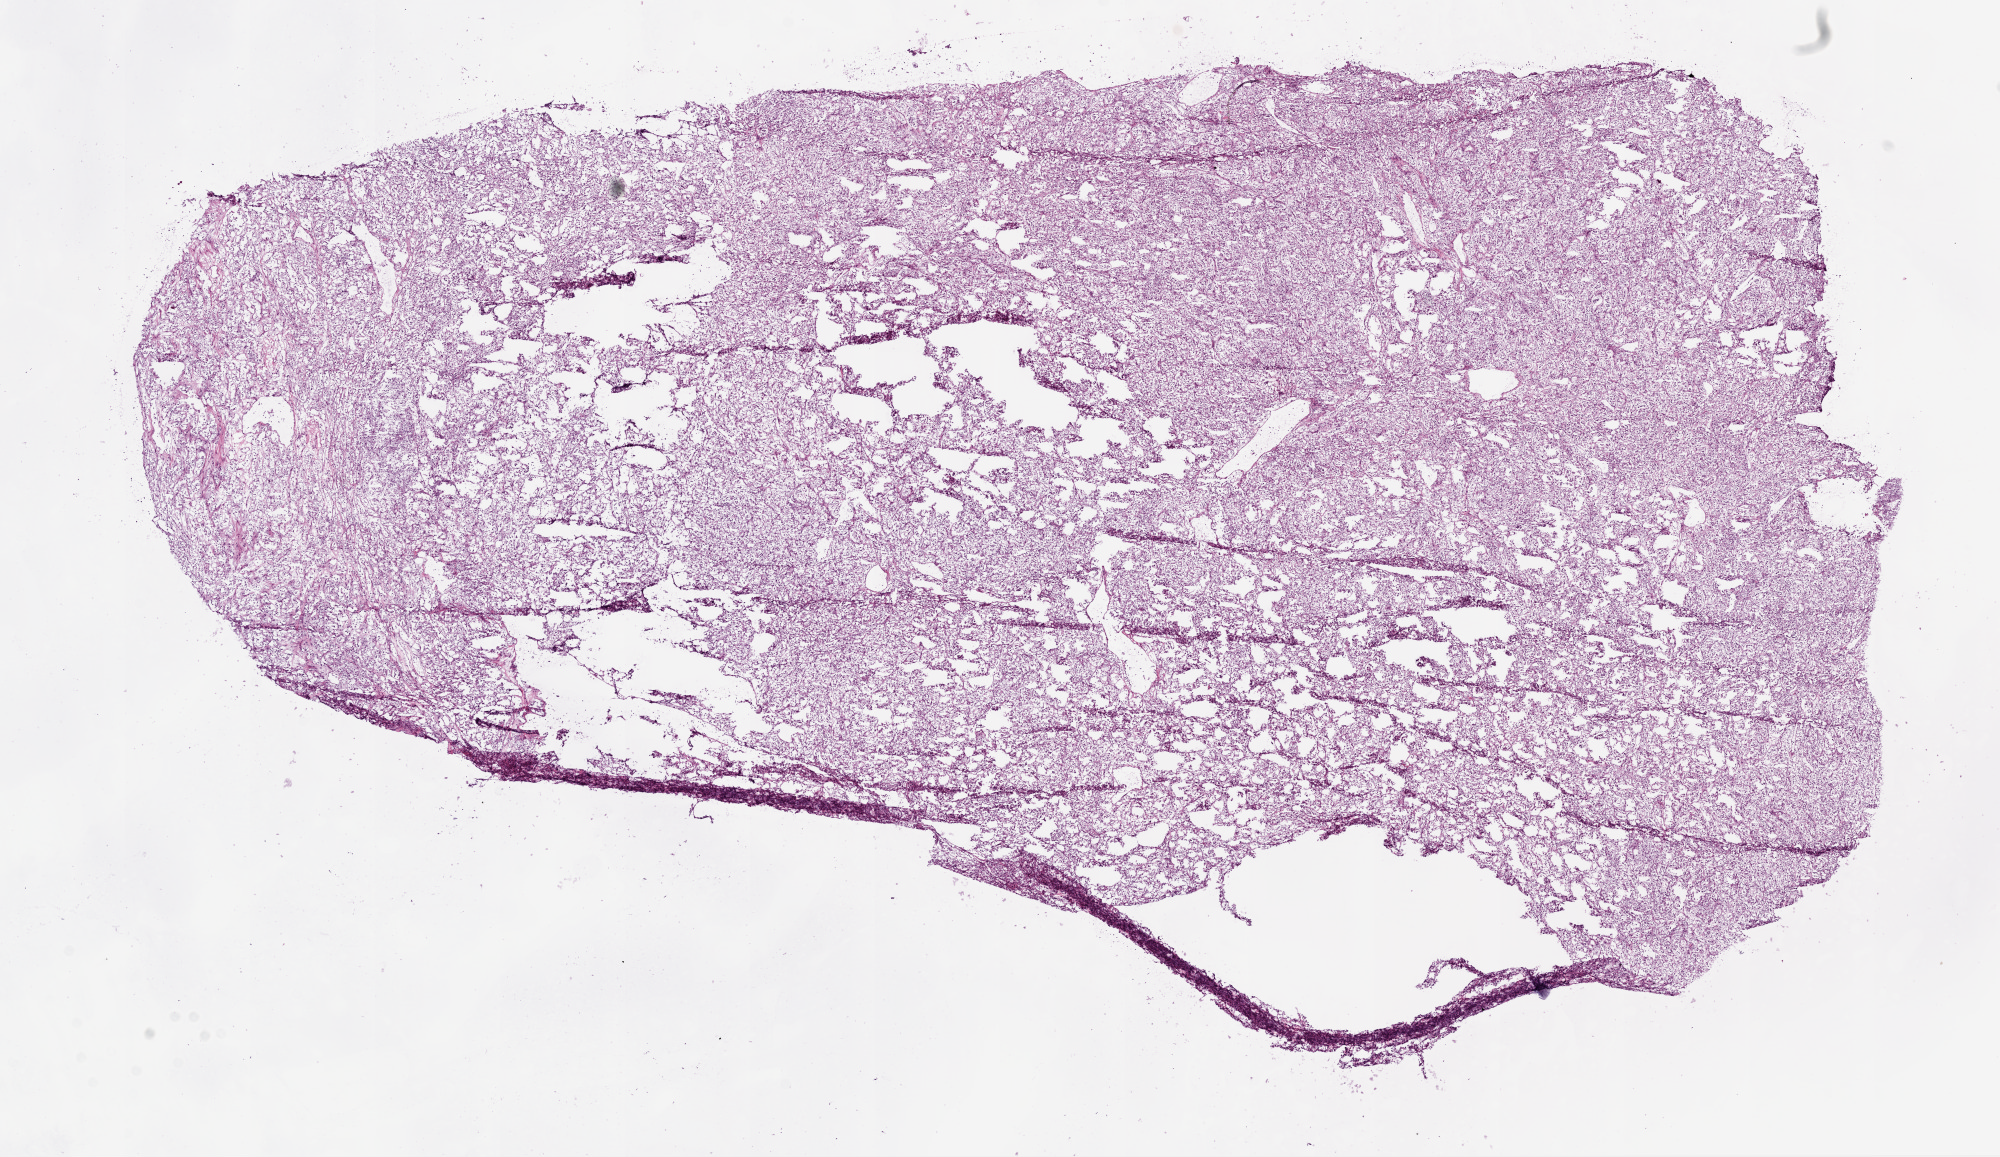
Digitized Hematoxylin and eosin (H&E) stained tissue section (whole slide), a low-resolution overview of the entire scanned area, about 16.0 x 9.3 mm (from a 20x scan); frozen section from the top of the tissue portion; primary tumour sample from the kidney. Male, age 71 years at initial diagnosis.
Histologic diagnosis: Clear cell adenocarcinoma, NOS.